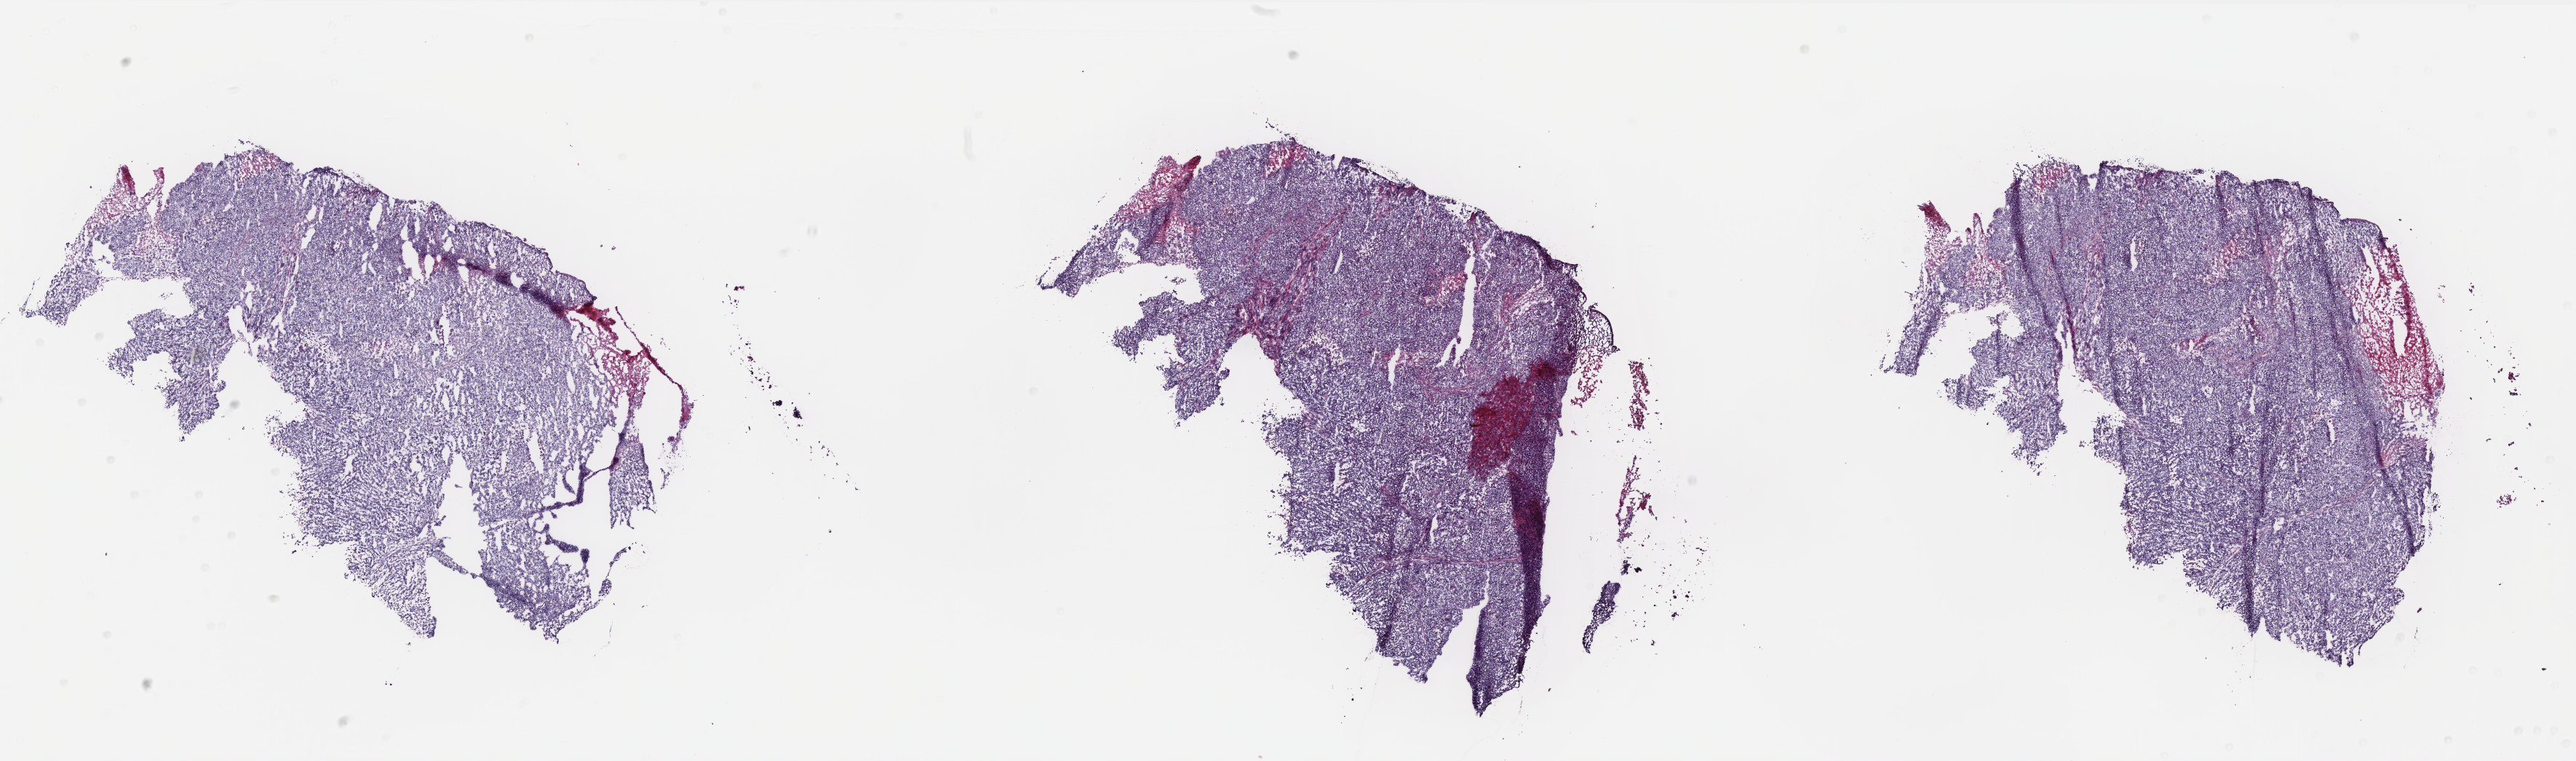
Digitized H&E tissue section (whole slide), low-resolution overview of the scanned area, about 28.4 x 8.4 mm; frozen section from the bottom of the tissue portion; uterus, primary tumour sample. Patient: female, age at initial diagnosis 57 years. Histologic grade: G3 (poorly differentiated). Composition of this section per pathologist review: tumour cells 85%, tumour nuclei 90%, normal cells 5%, stromal cells 0%, necrosis 10%. Infiltration values recorded for this section: lymphocyte infiltration 20%, monocyte infiltration 0%, neutrophil infiltration 10%.
• pathologic diagnosis: Serous cystadenocarcinoma, NOS
• FIGO stage: IIIB